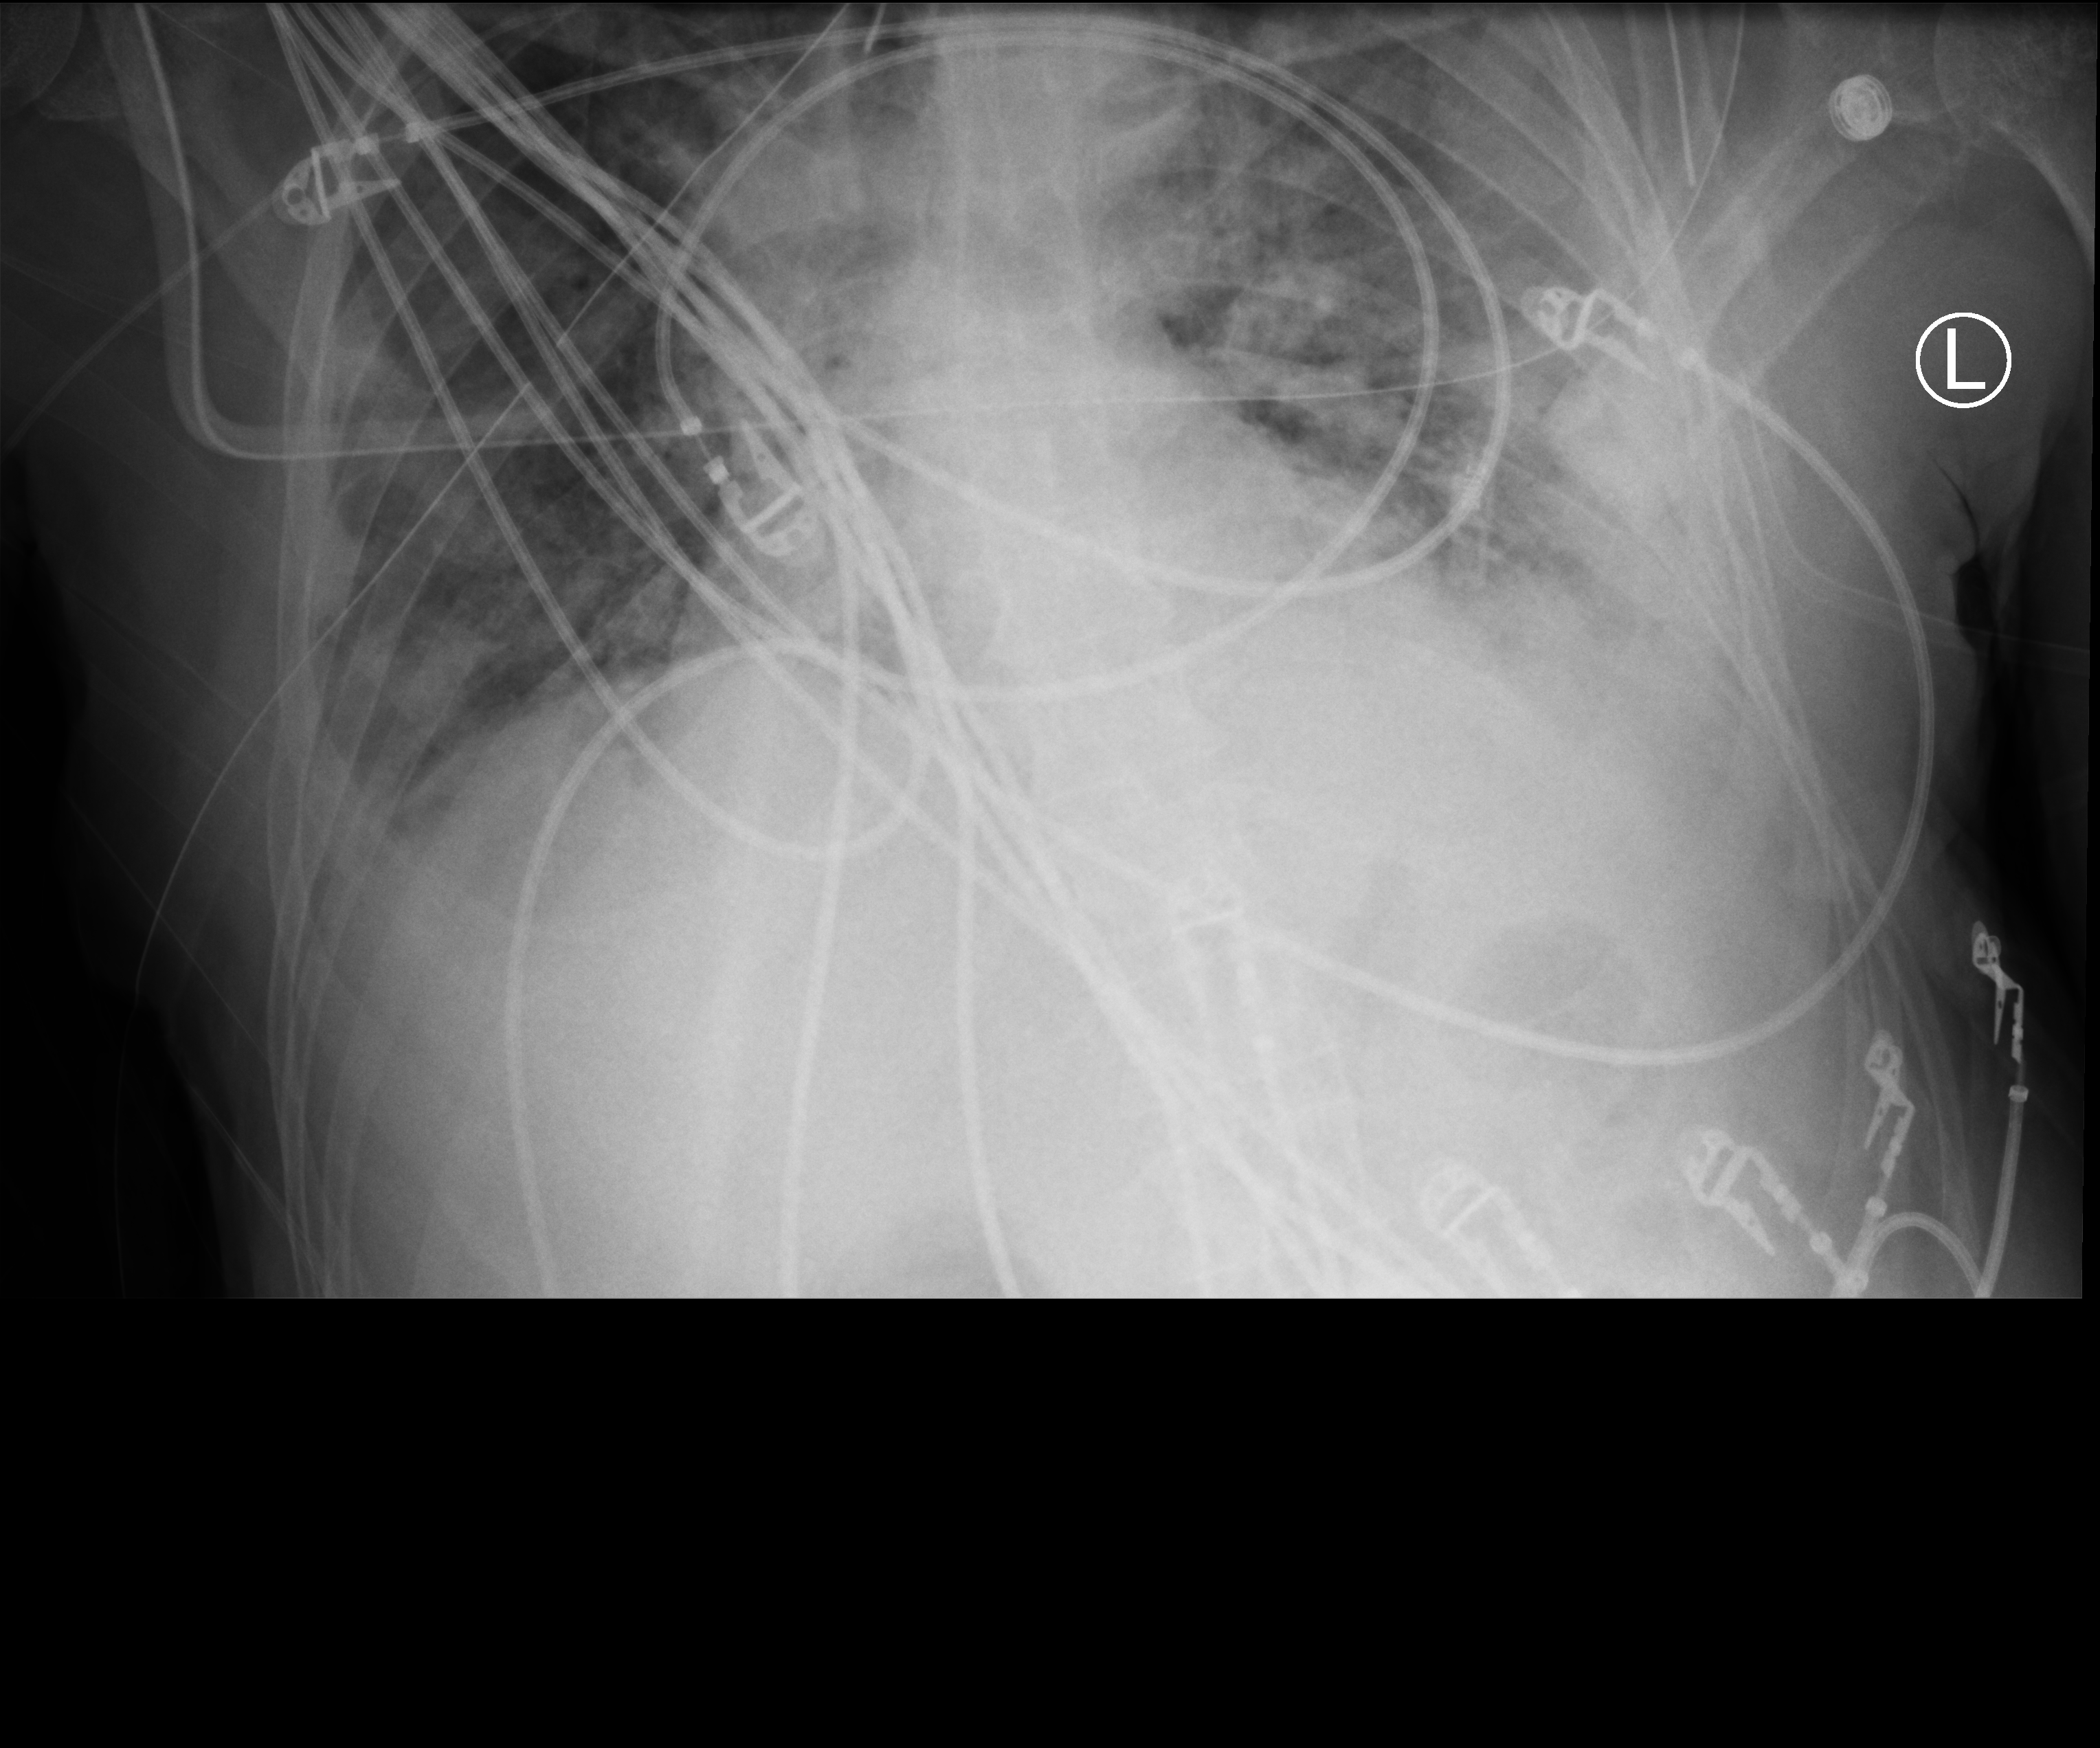
Chest X-ray (portable); anteroposterior (AP) projection. Male patient hospitalised with COVID-19, age 18–59 years.
Hospital-stay facts (about this admission, not read from this image; timing relative to this image not recorded): admitted to intensive care during this hospital stay: yes.